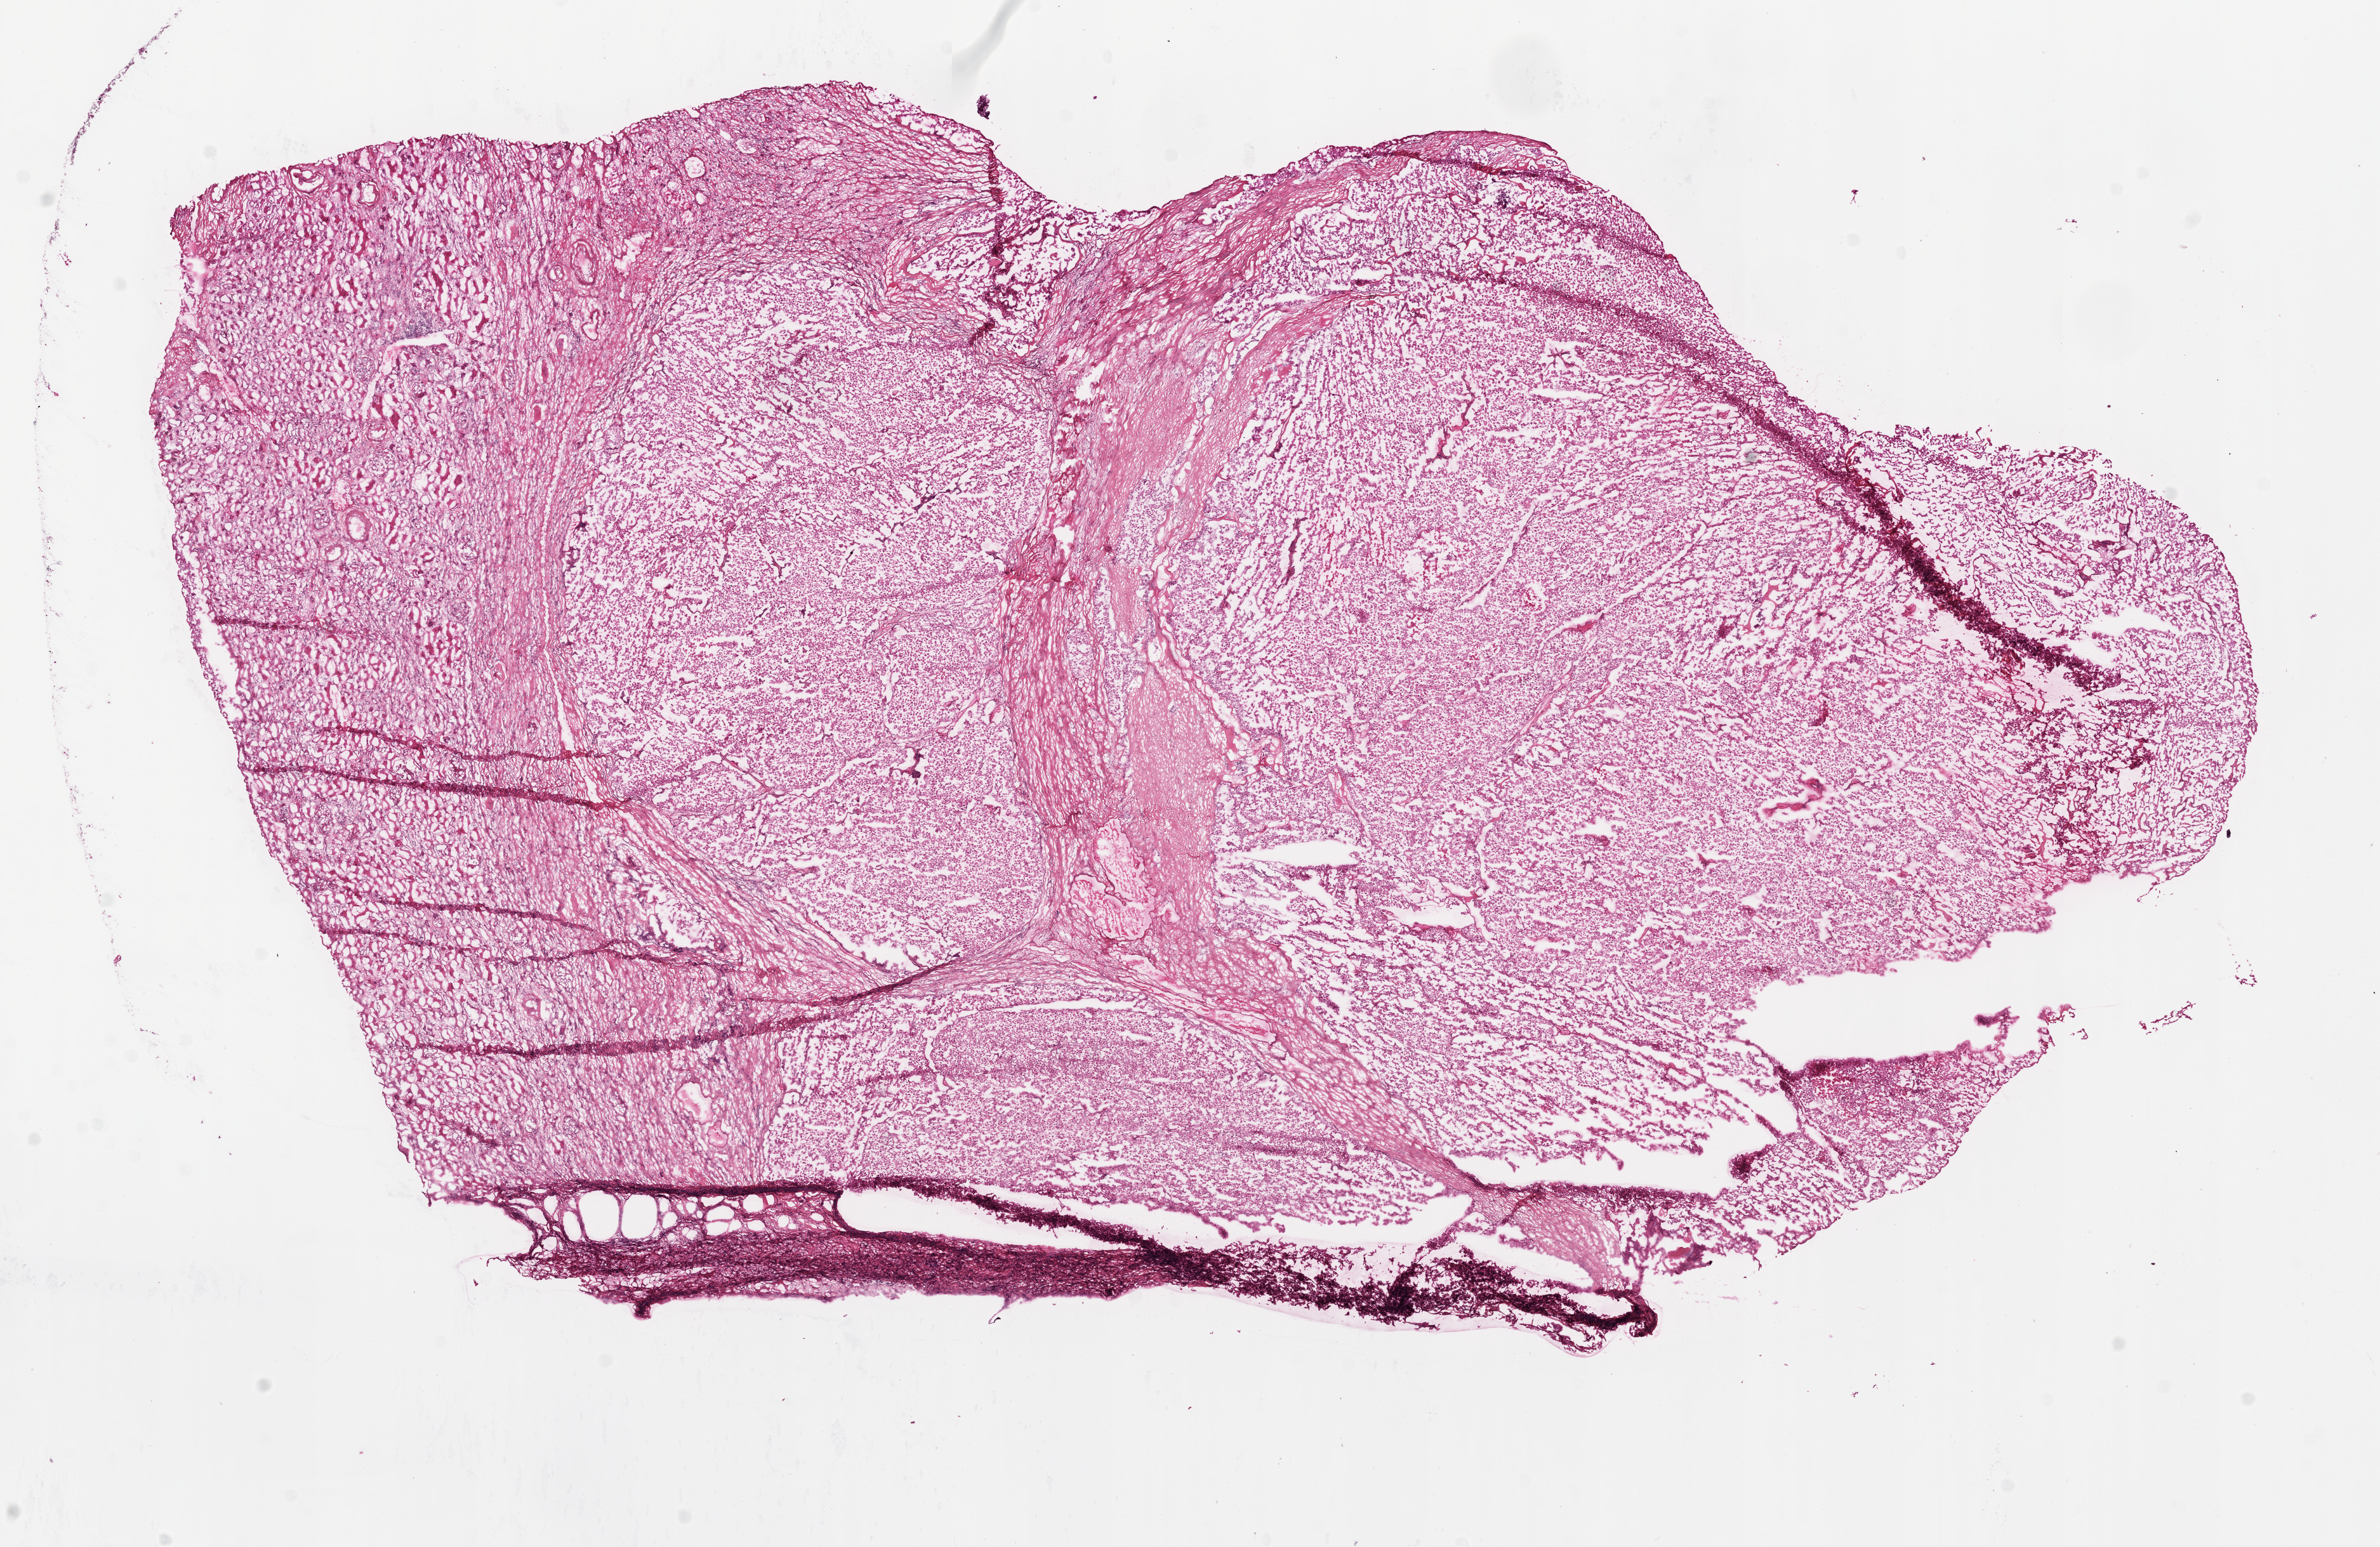
H&E whole-slide image, a low-resolution overview of the entire scanned area, about 15.0 x 9.8 mm, frozen section from the top of the tissue portion, primary tumour sample from the kidney. Patient: female, age at initial diagnosis 71 years.
Pathologic diagnosis: Clear cell adenocarcinoma, NOS.